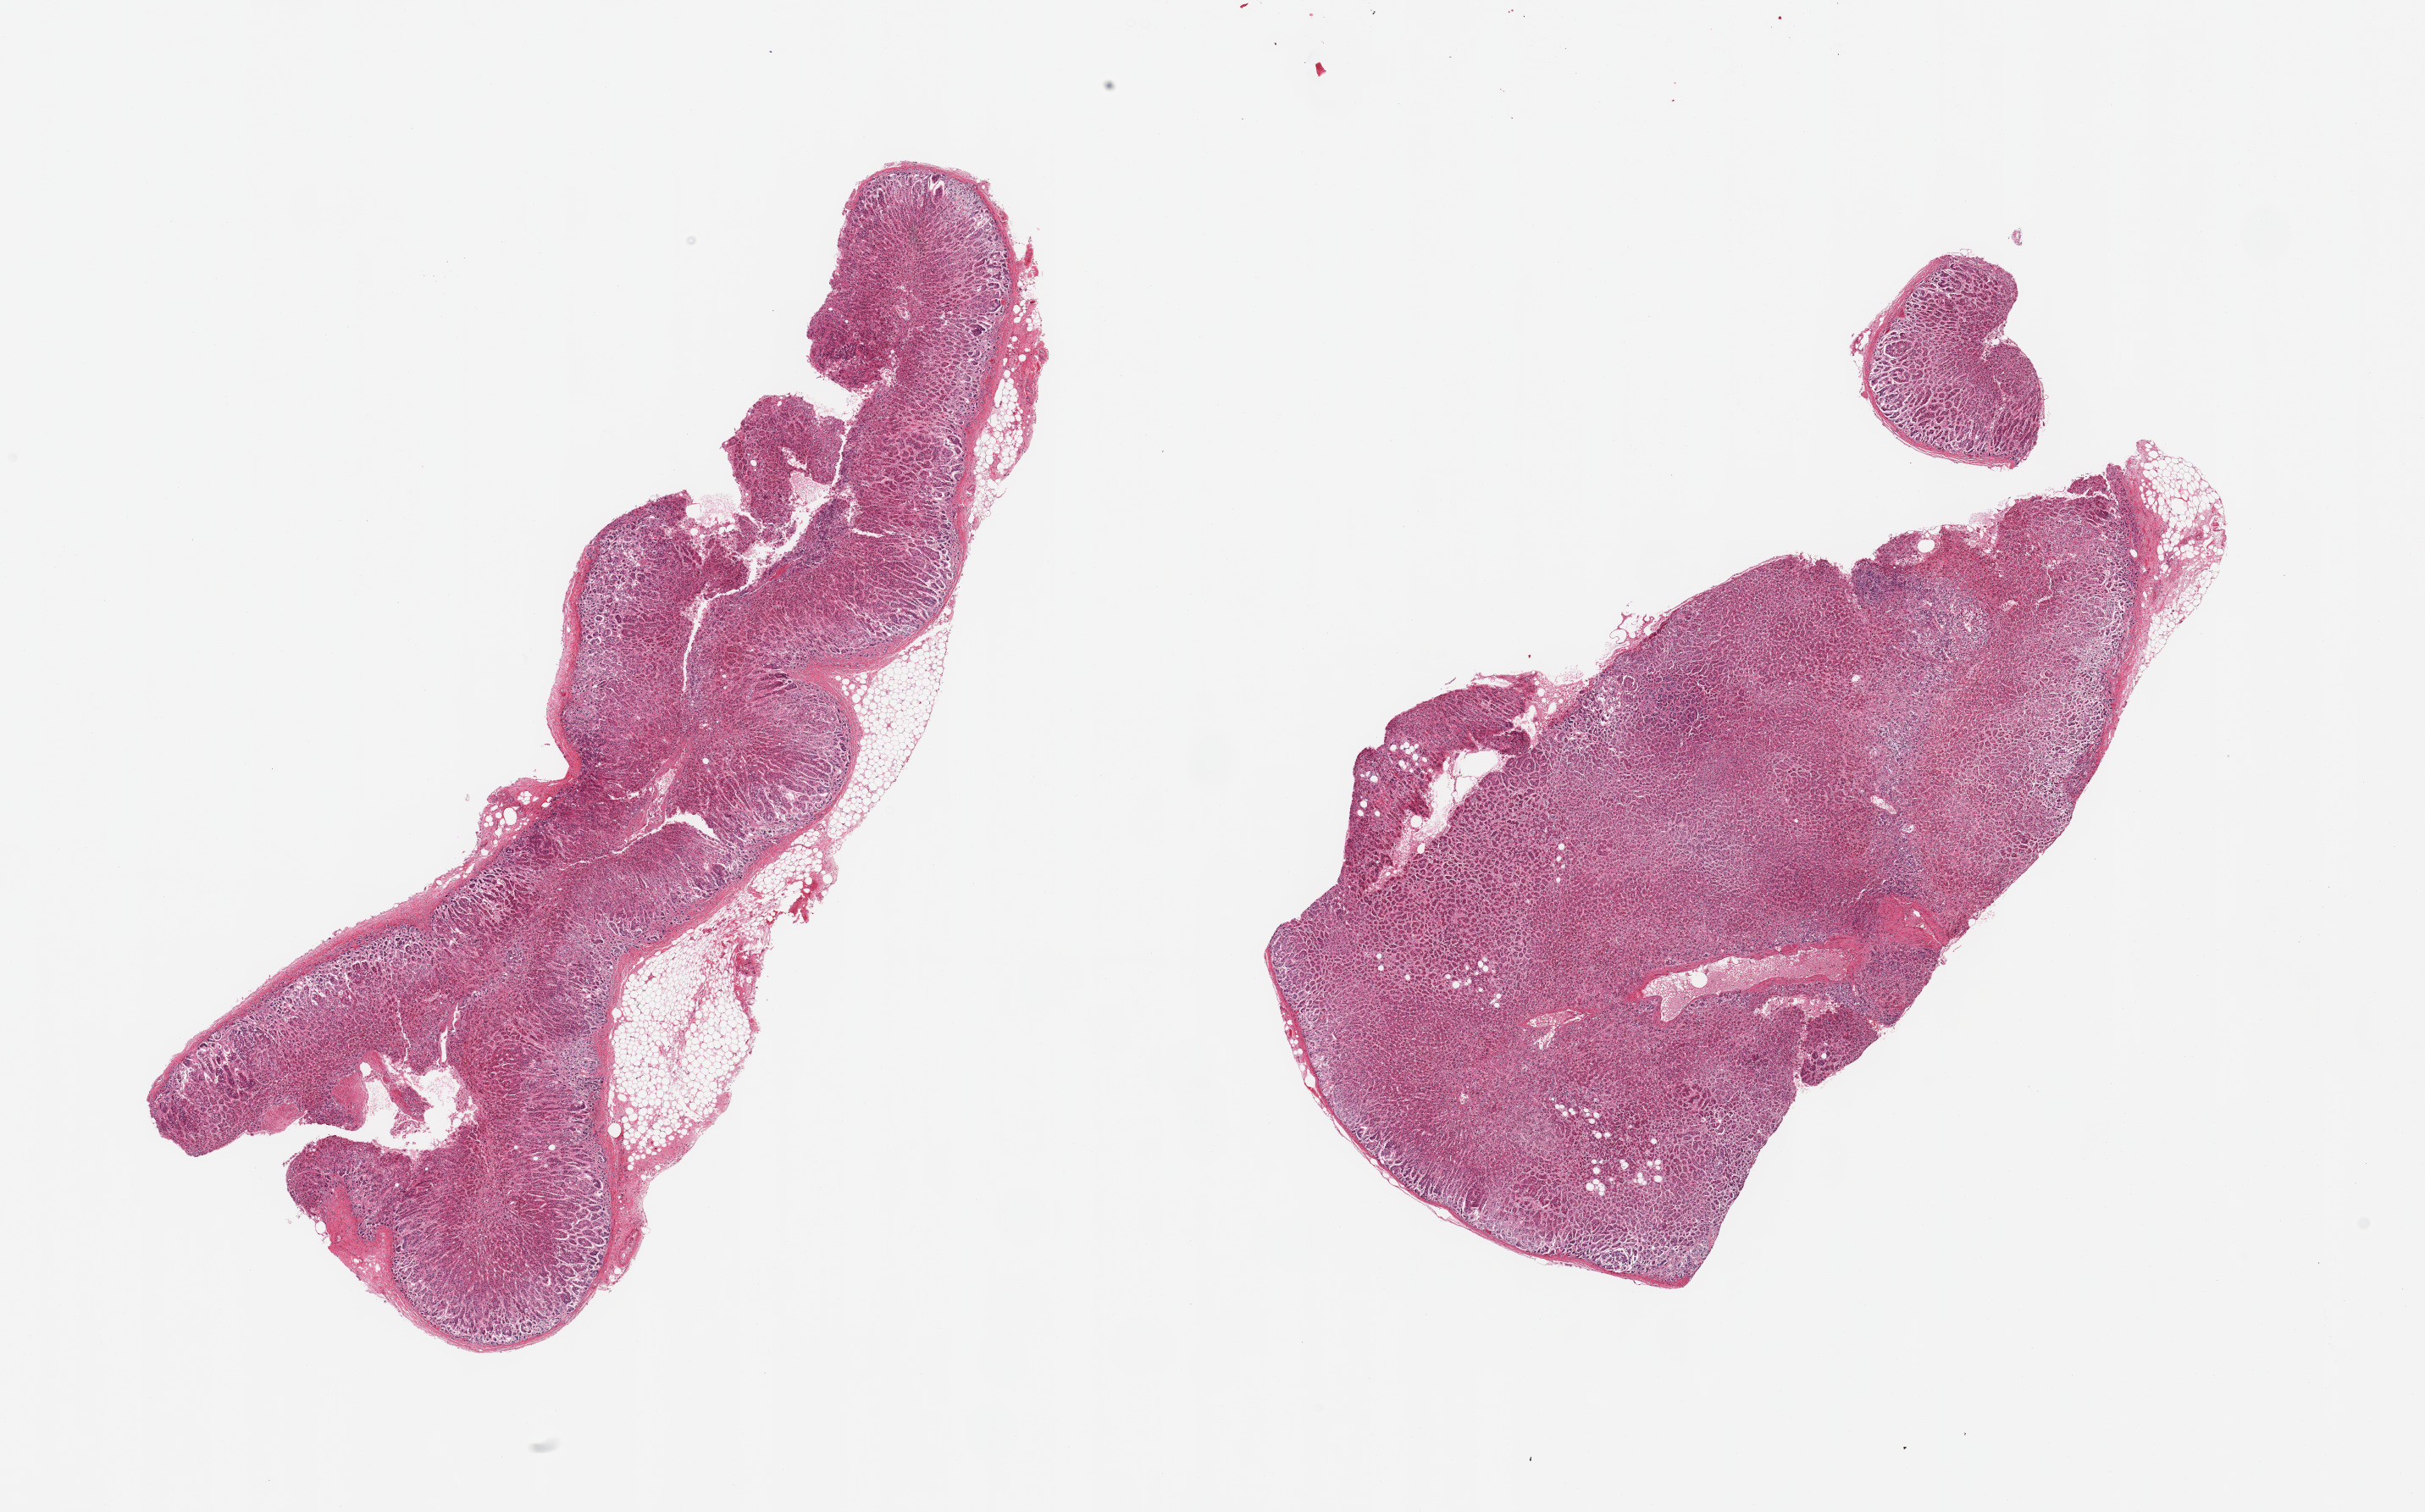
Digitized hematoxylin and eosin (H&E)-stained section, brightfield, low-resolution overview of the scanned area, about 22.6 x 14.1 mm; PAXgene-fixed paraffin-embedded (PFPE) section; target tissue: adrenal gland; donor tissue sample. Female donor.
Reviewer comment on this tissue sample: 2 pieces, cortex, focal adherent fat up to ~1 mm.